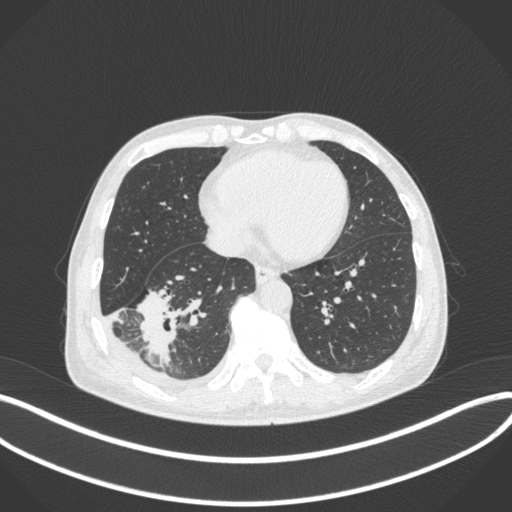
Chest CT, one axial slice. Slice 127 of 385 in the series (ordered by position). Reconstruction kernel B31f. Lung window (W 1500 / L -600 HU). 512 × 512 image matrix, field of view 400 × 400 mm. Male patient, age 64 years. From the clinical record (not read from this slice): clinical TNM (as recorded): T3 N0 M0; histopathological grade: G2-3.
Structures marked on this image (bounding box drawn by a radiologist):
- lung tumour (recorded histology: adenocarcinoma): bounding box <134,286,181,366> (left, top, right, bottom; pixels)